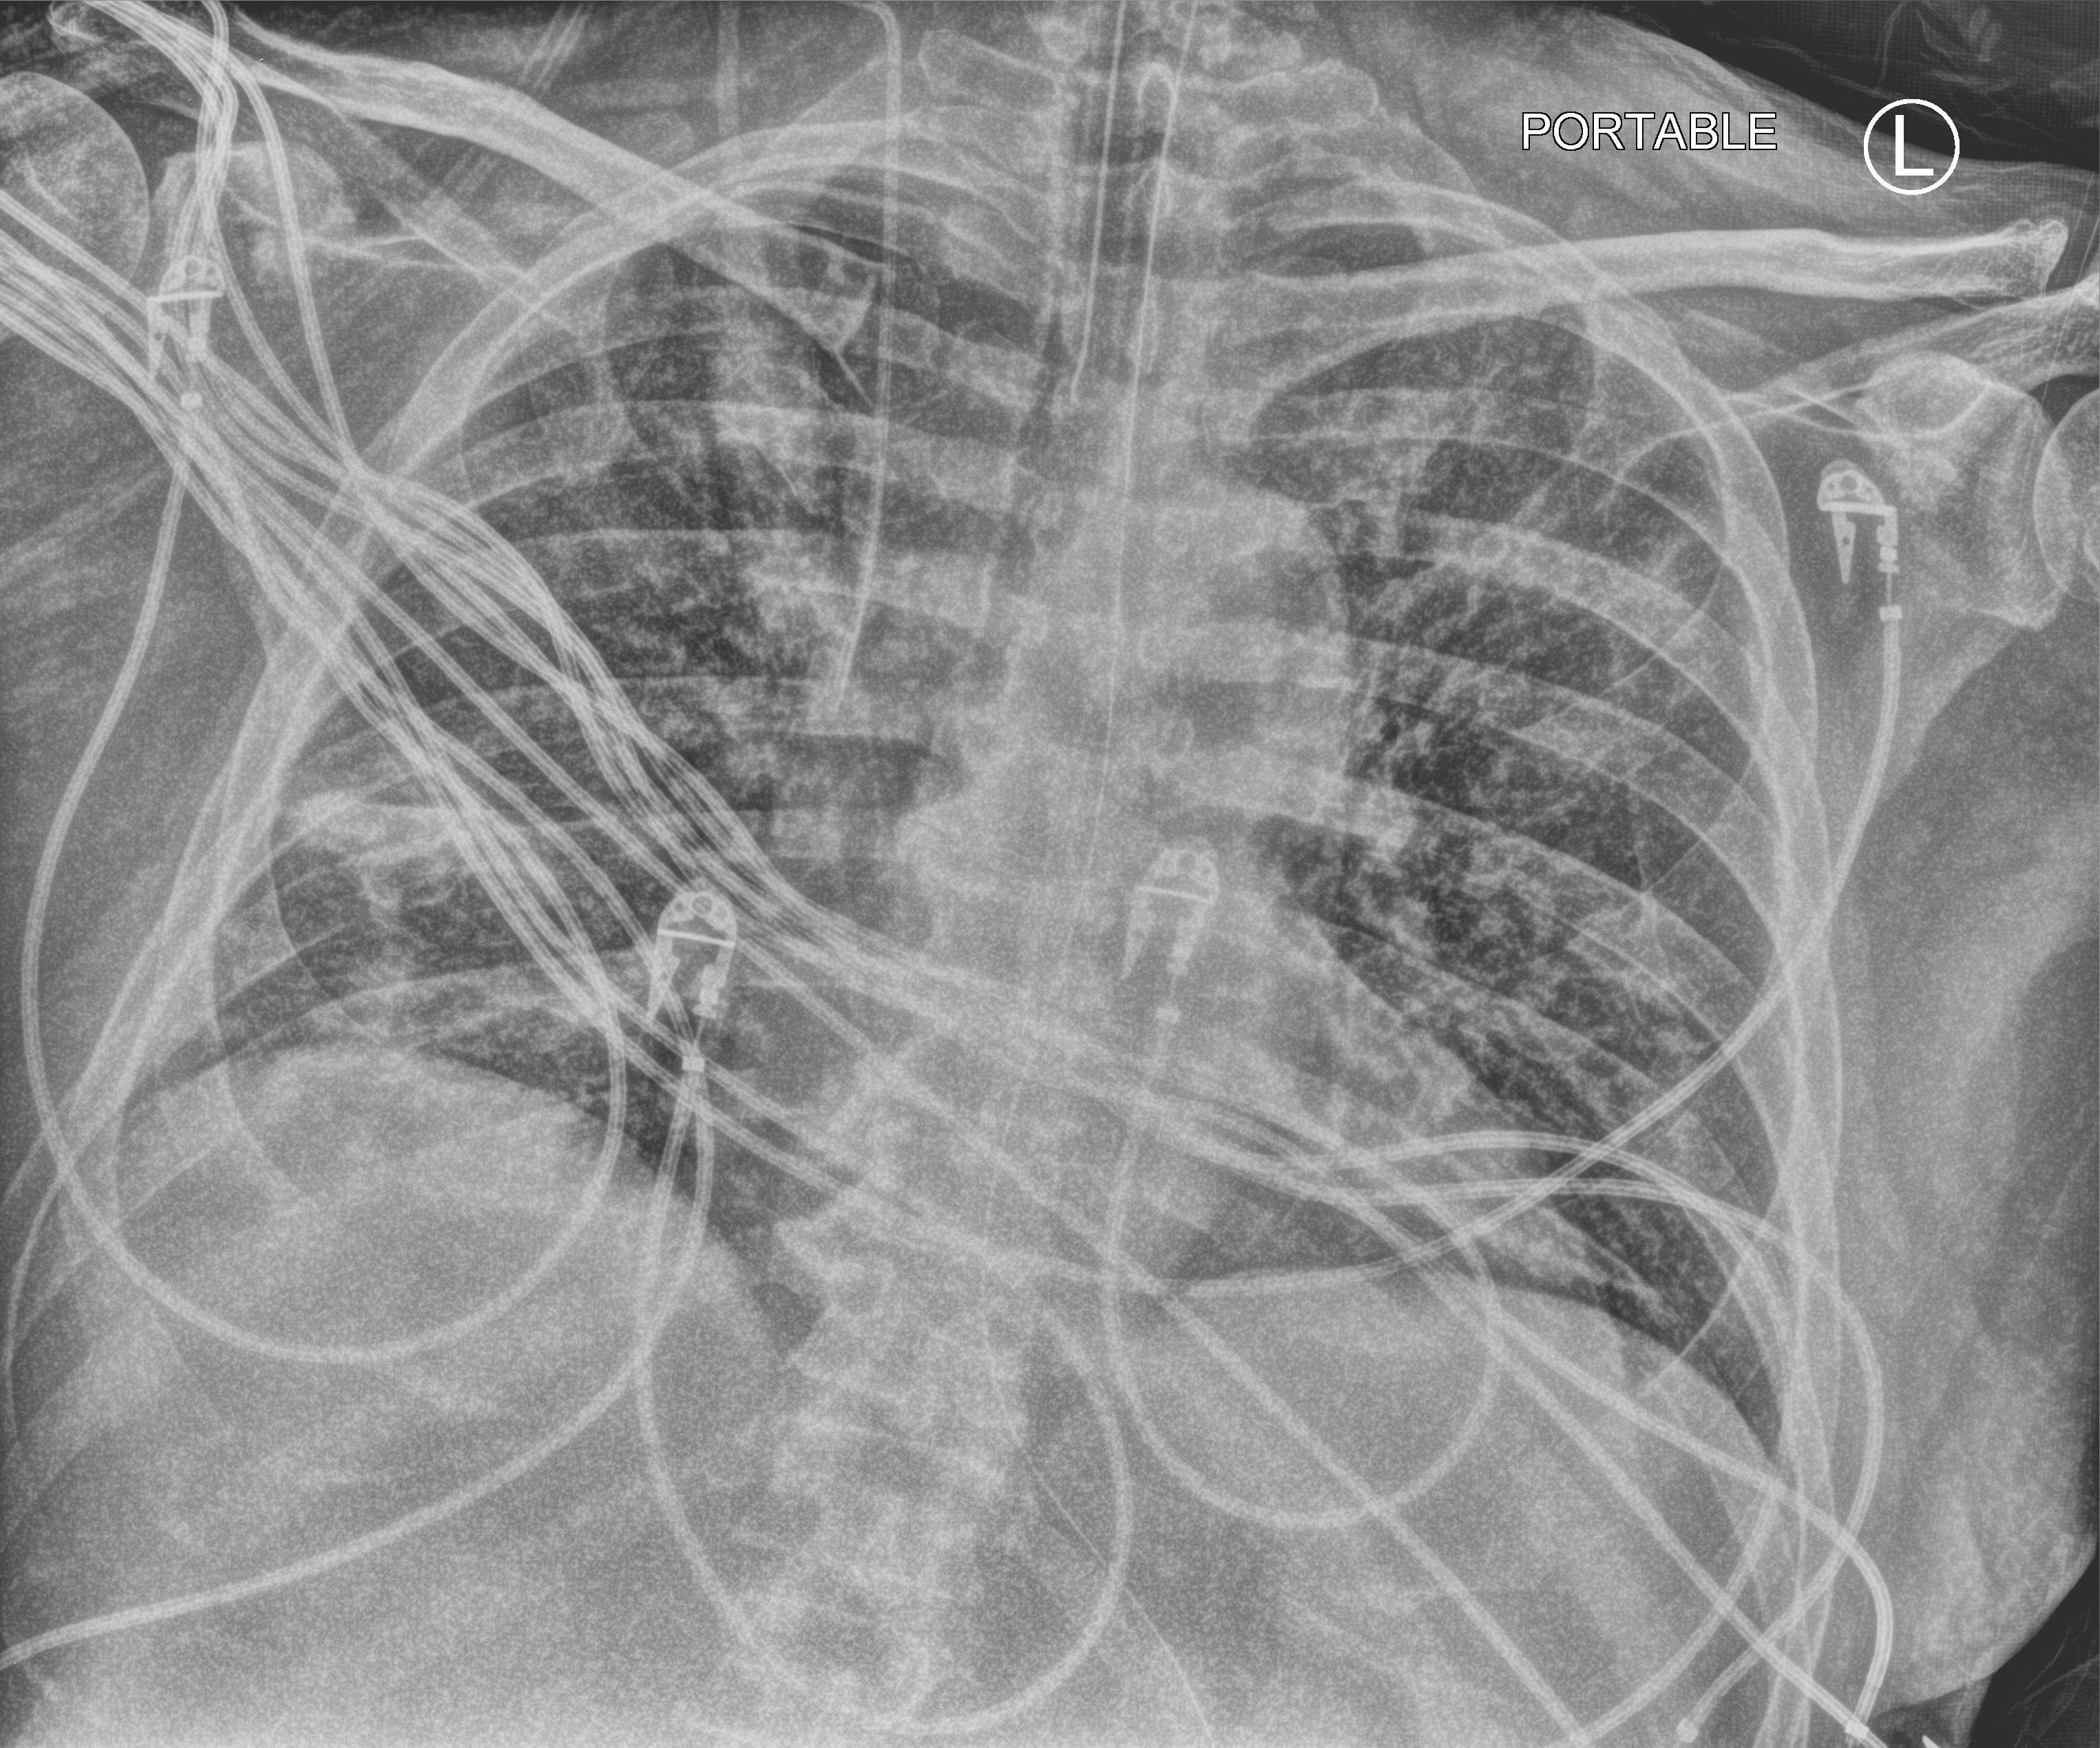
Portable chest radiograph, anteroposterior (AP) projection. Patient hospitalised with COVID-19; male, aged 60–74 years.
From the hospital-stay record, not from the radiograph (when in the stay this image was taken is not recorded):
- admitted to intensive care during this hospital stay: yes
- mechanically ventilated during this hospital stay: yes
- hypertension (admission record): yes